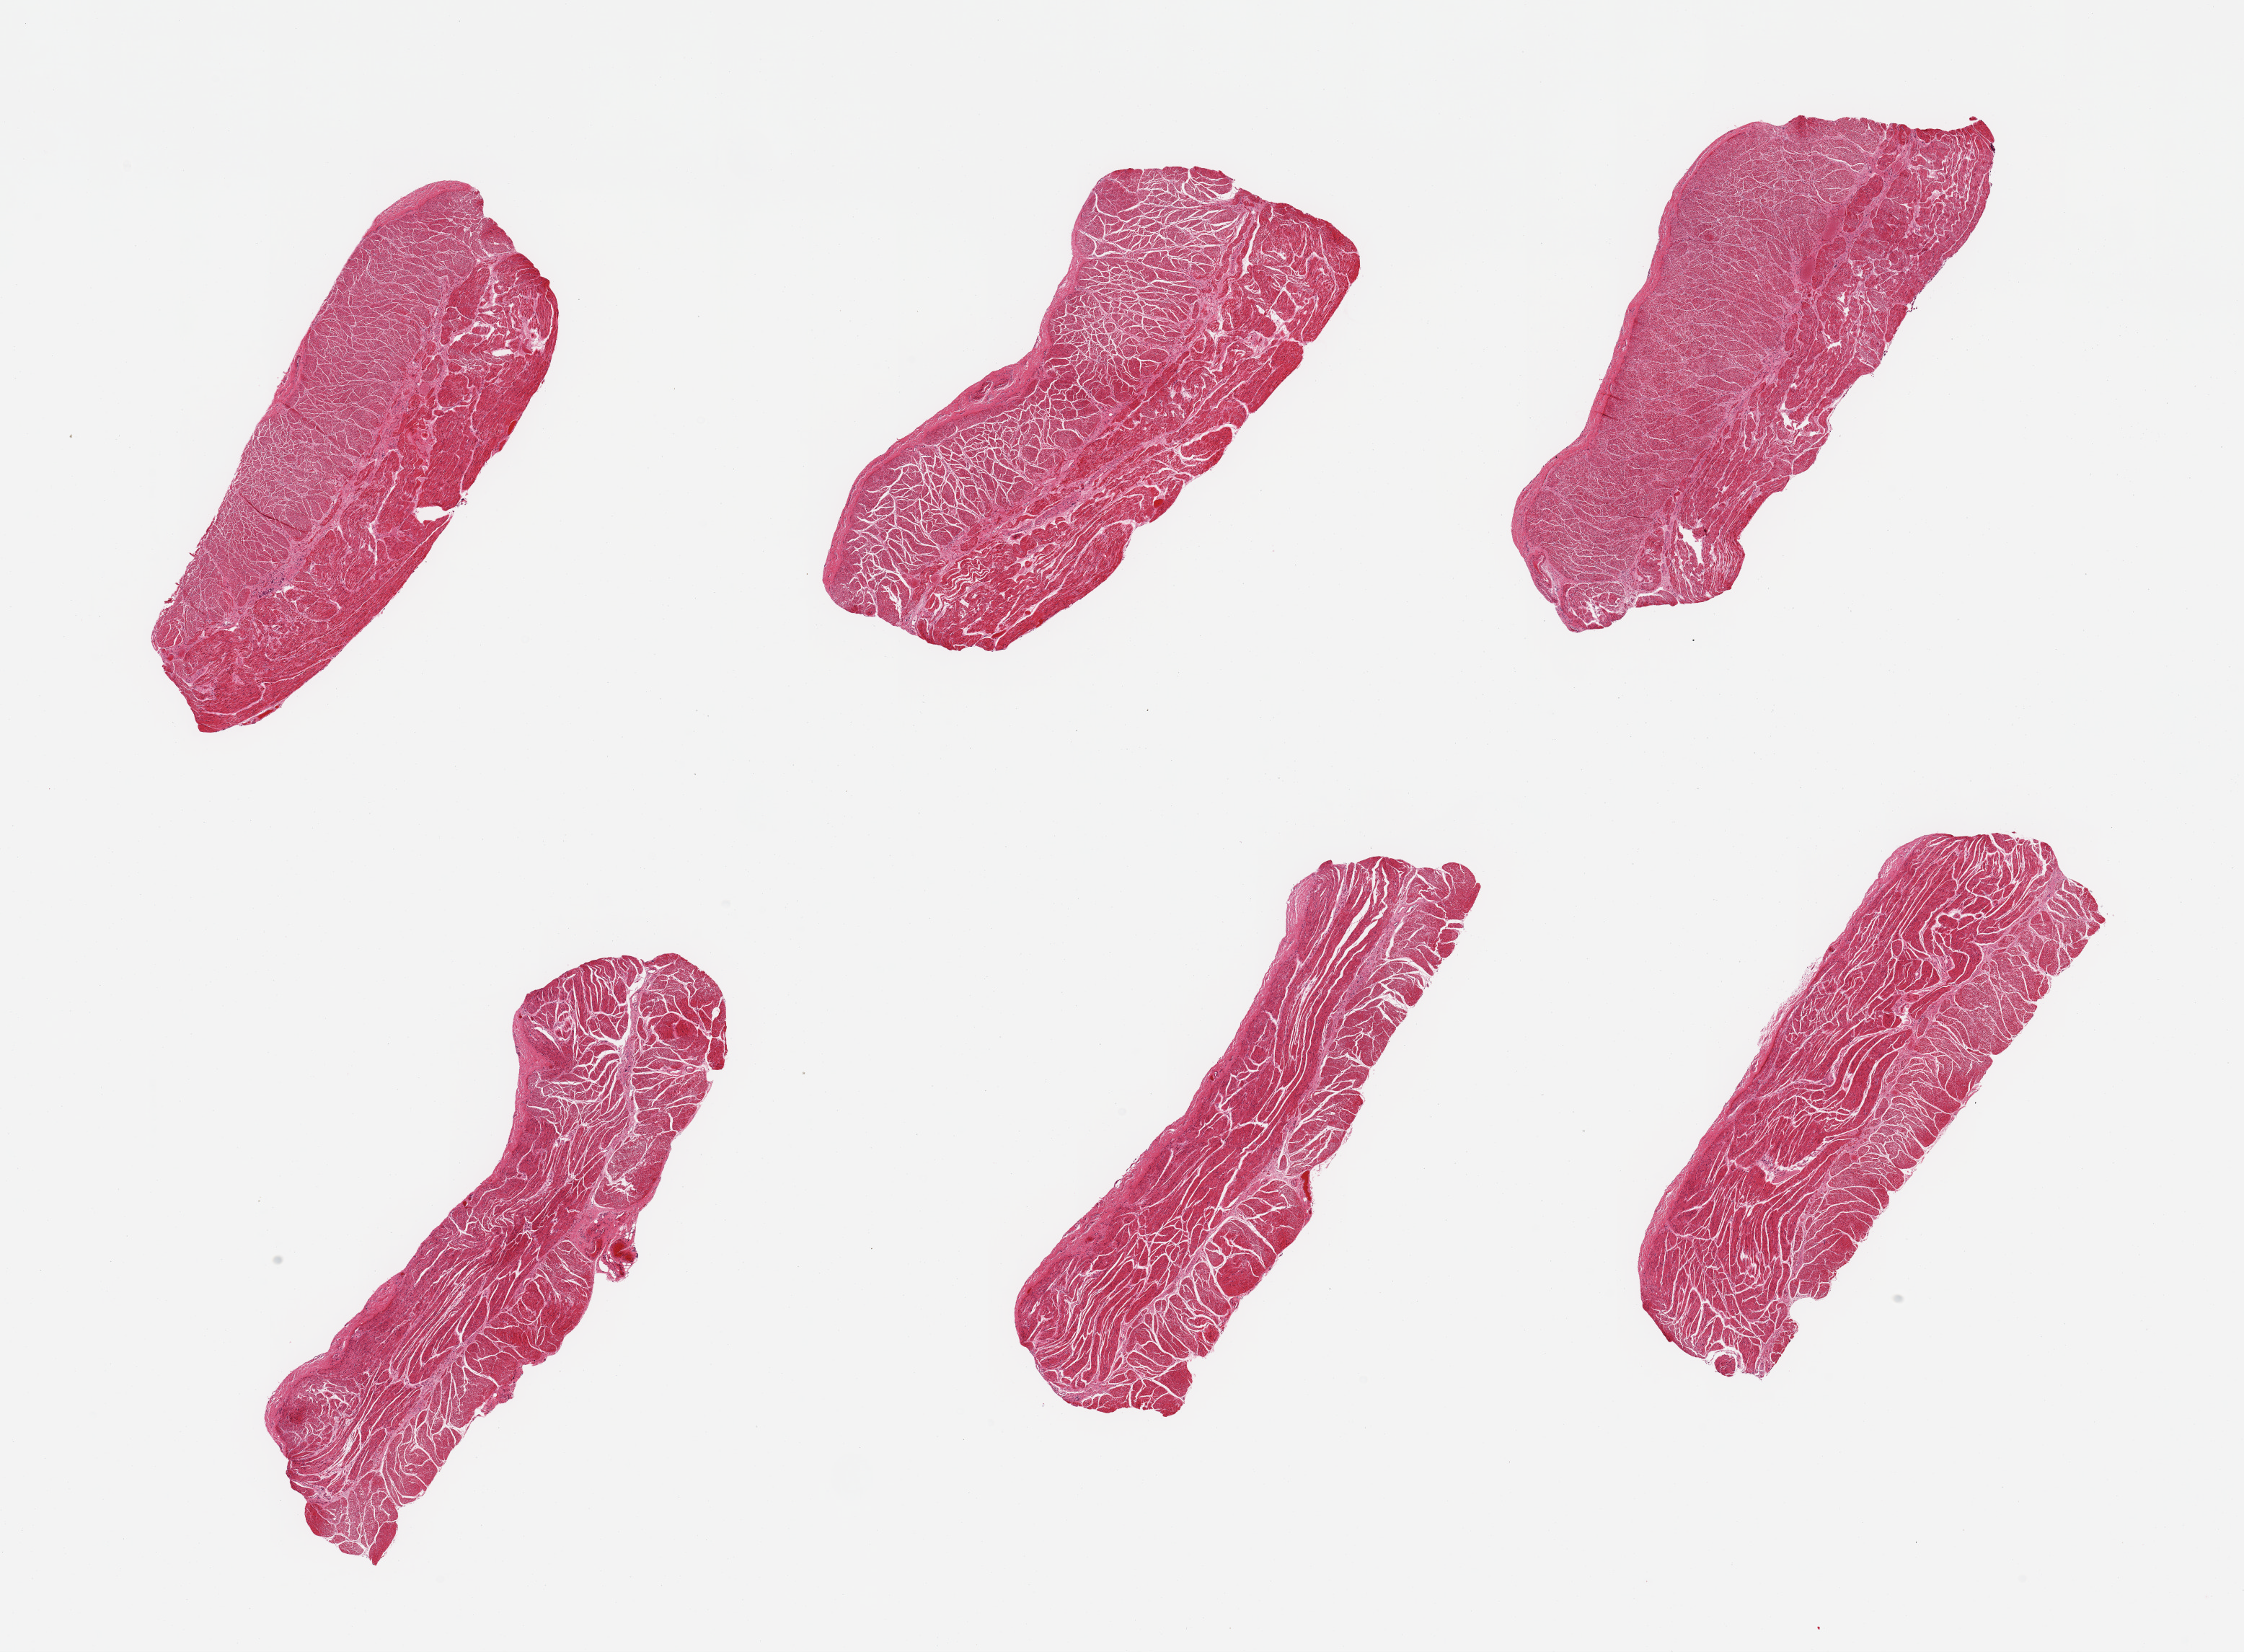
Whole-slide image, haematoxylin and eosin stain — whole scanned area (about 24.6 x 18.1 mm, acquisition: 20x scan) shown as a low-resolution overview, PAXgene-fixed, paraffin-embedded tissue, target tissue: esophageal muscle, donor tissue sample. Donor sex: male.
Pathologist's review note for this sample: 6 pieces; well trimmed muscle.